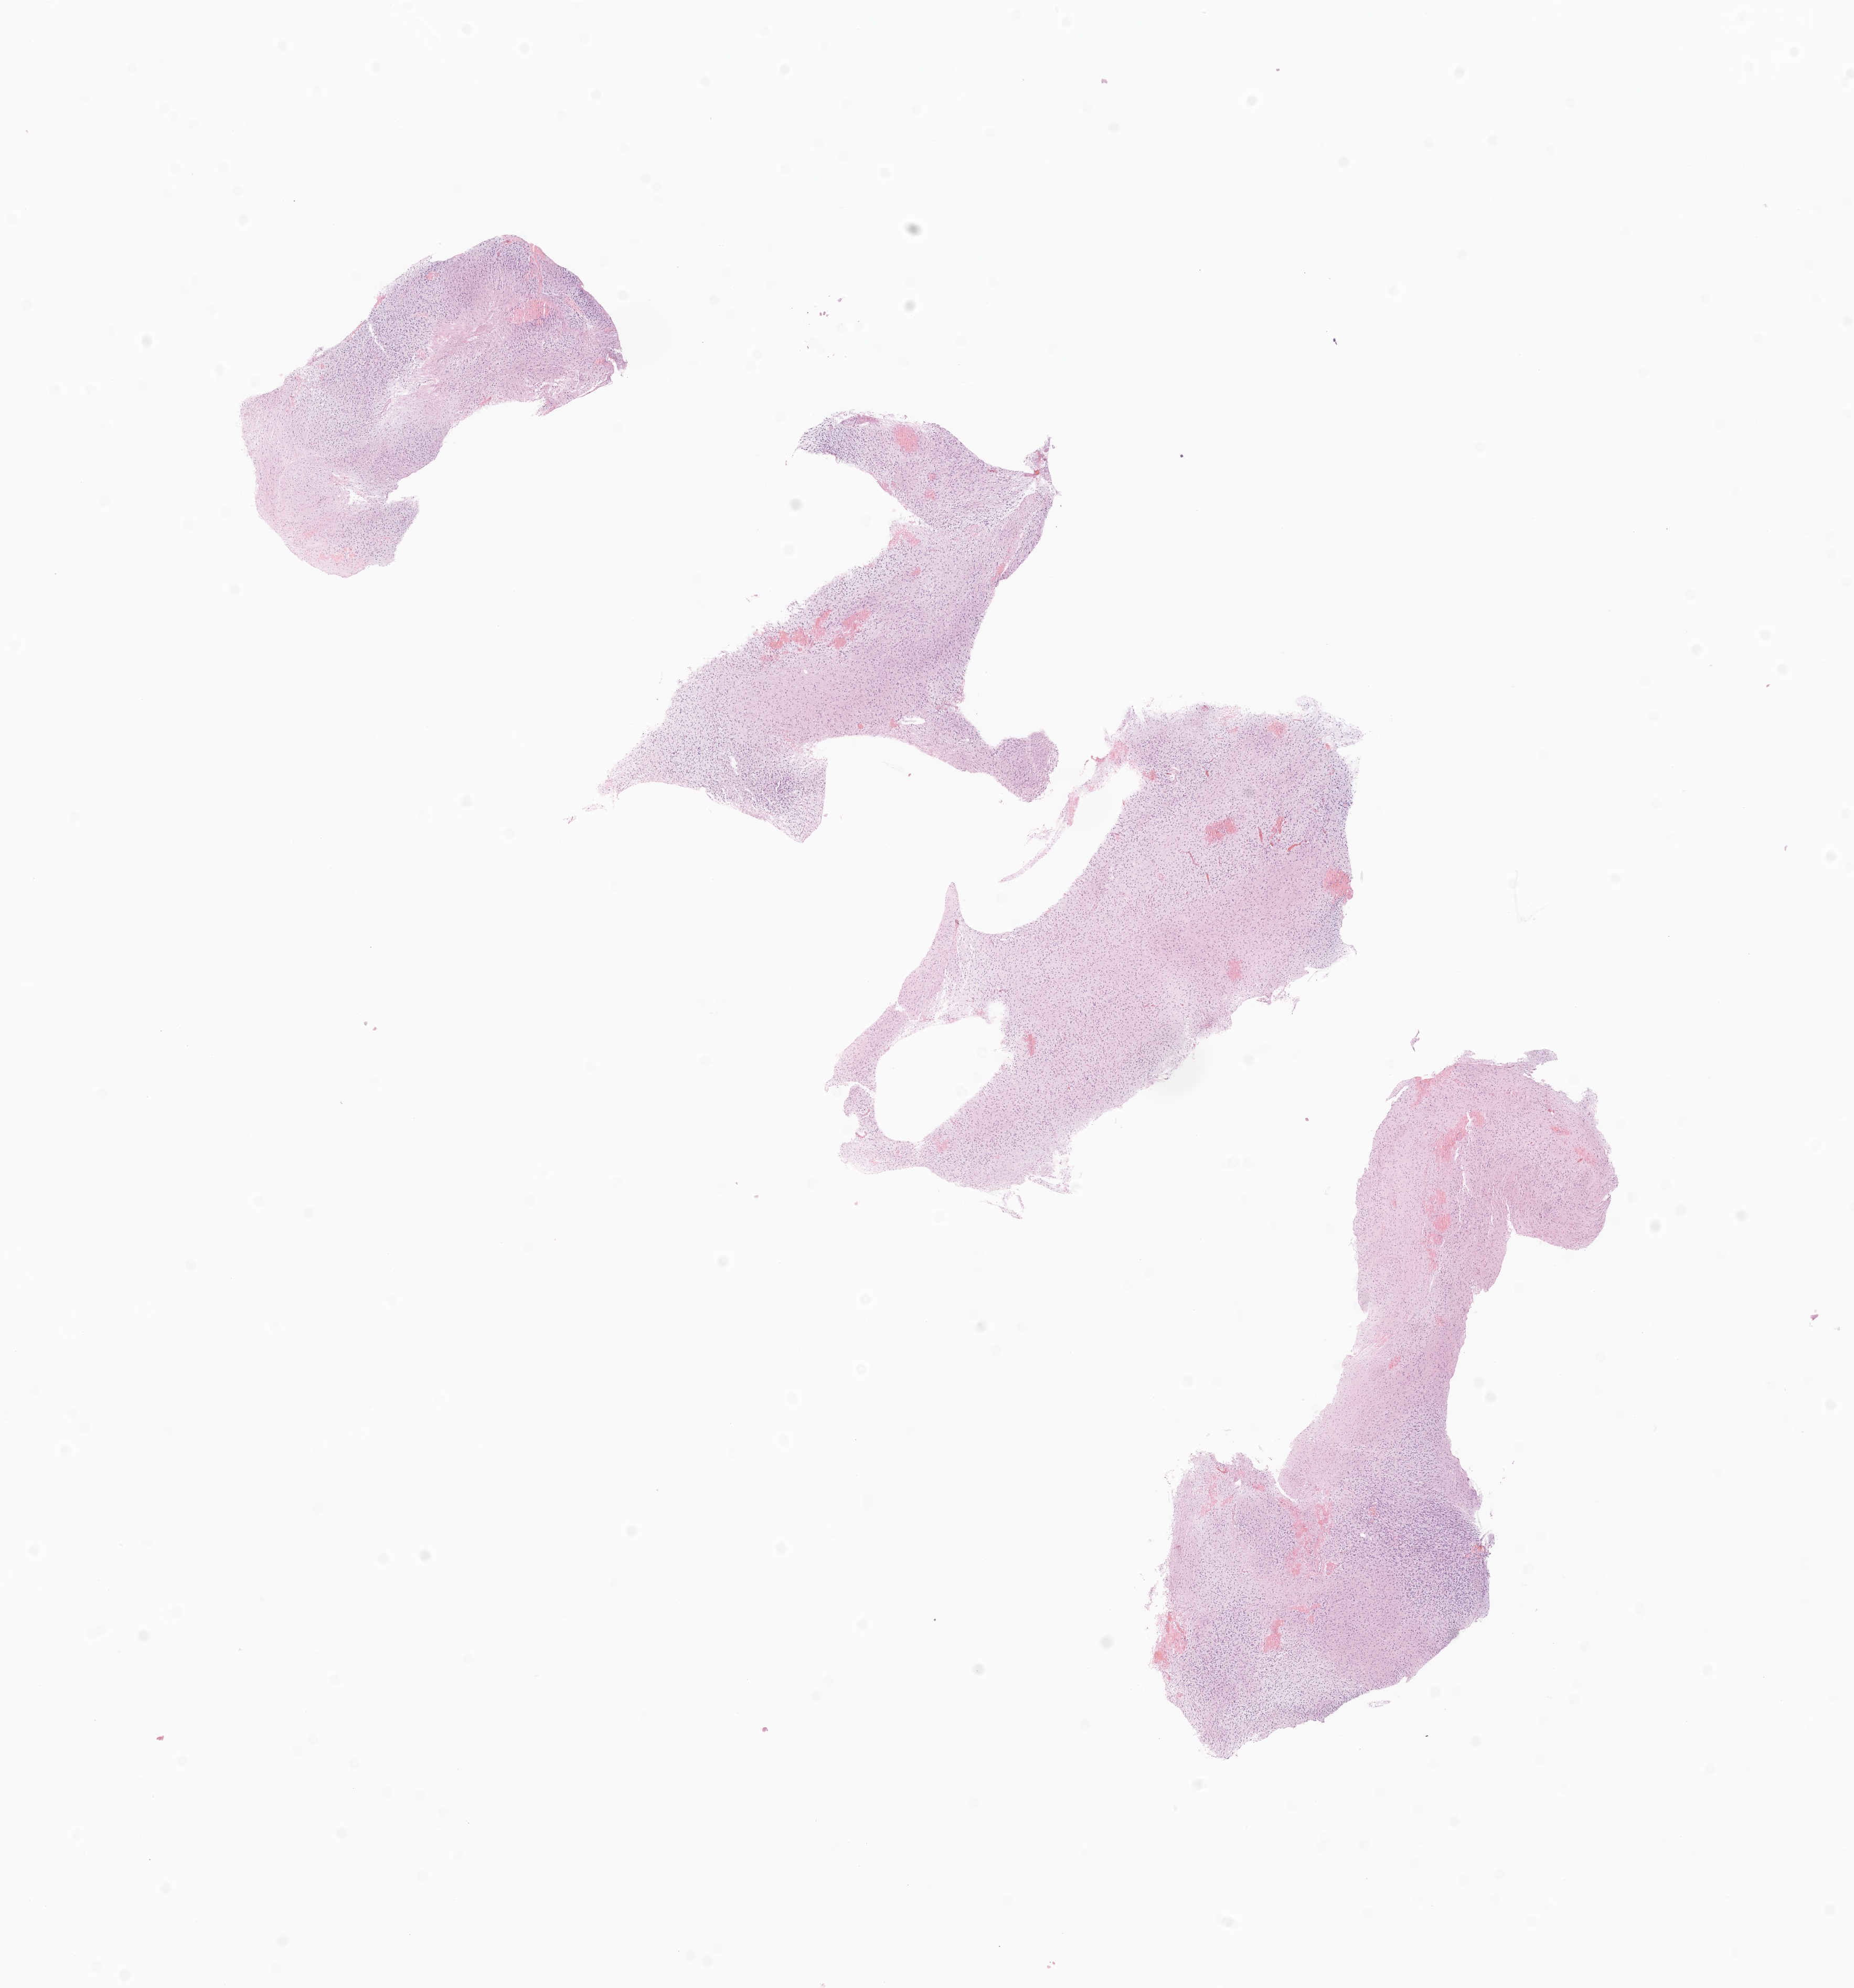
Digitized hematoxylin and eosin (H&E)-stained section of tumor tissue from the brain, low-resolution overview of the scanned area, about 14.9 x 16.0 mm; formalin-fixed, paraffin-embedded (FFPE) tissue. Patient: male, age 64 months (5 years 4 months).
Recorded diagnosis: Glioma, malignant.